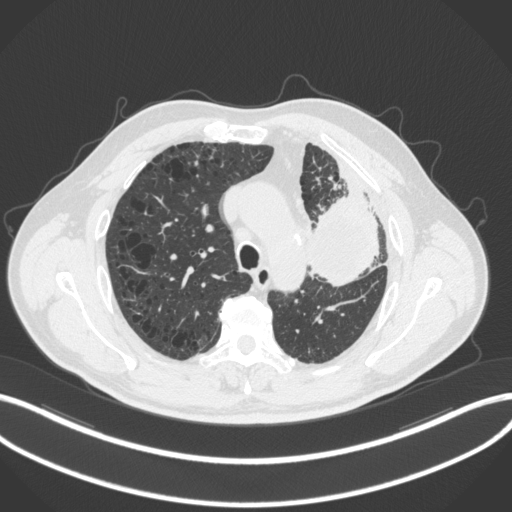
Chest CT, one axial slice; position 213 of 286 along the scan axis; reconstruction kernel B31f; 120 kVp; lung window (W 1500 / L -600 HU); 1 mm slice thickness; 512 × 512 image matrix, field of view 400 × 400 mm. Male patient, age 68 years. From the clinical record (not read from this slice): clinical TNM (as recorded): T3 N3 M1.
Outlined on this slice (bounding box drawn by a radiologist):
- lung tumour (recorded histology: adenocarcinoma): box from (x=301, y=178) to (x=382, y=289) px